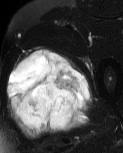
MRI of an extremity soft-tissue mass, one axial slice; slice 36 of 60 in the series (ordered by position); T2-weighted fat-saturated; MR volume resampled by the dataset authors to the PET/CT grid (not the native acquisition matrix); 3.27 mm slice thickness; 123 × 153 image matrix. Male patient. Case-level facts recorded for this patient, not image findings: histological type: pleiomorphic liposarcoma; grade: high; site of the primary tumour: left thigh.
Outlined on this slice (expert contour drawn on MRI and transferred to this co-registered scan by the dataset authors):
- gross tumour volume including surrounding oedema: bounding box [x1, y1, x2, y2] px = [6, 47, 92, 140]
- gross tumour volume (mass): [8, 49, 91, 128]